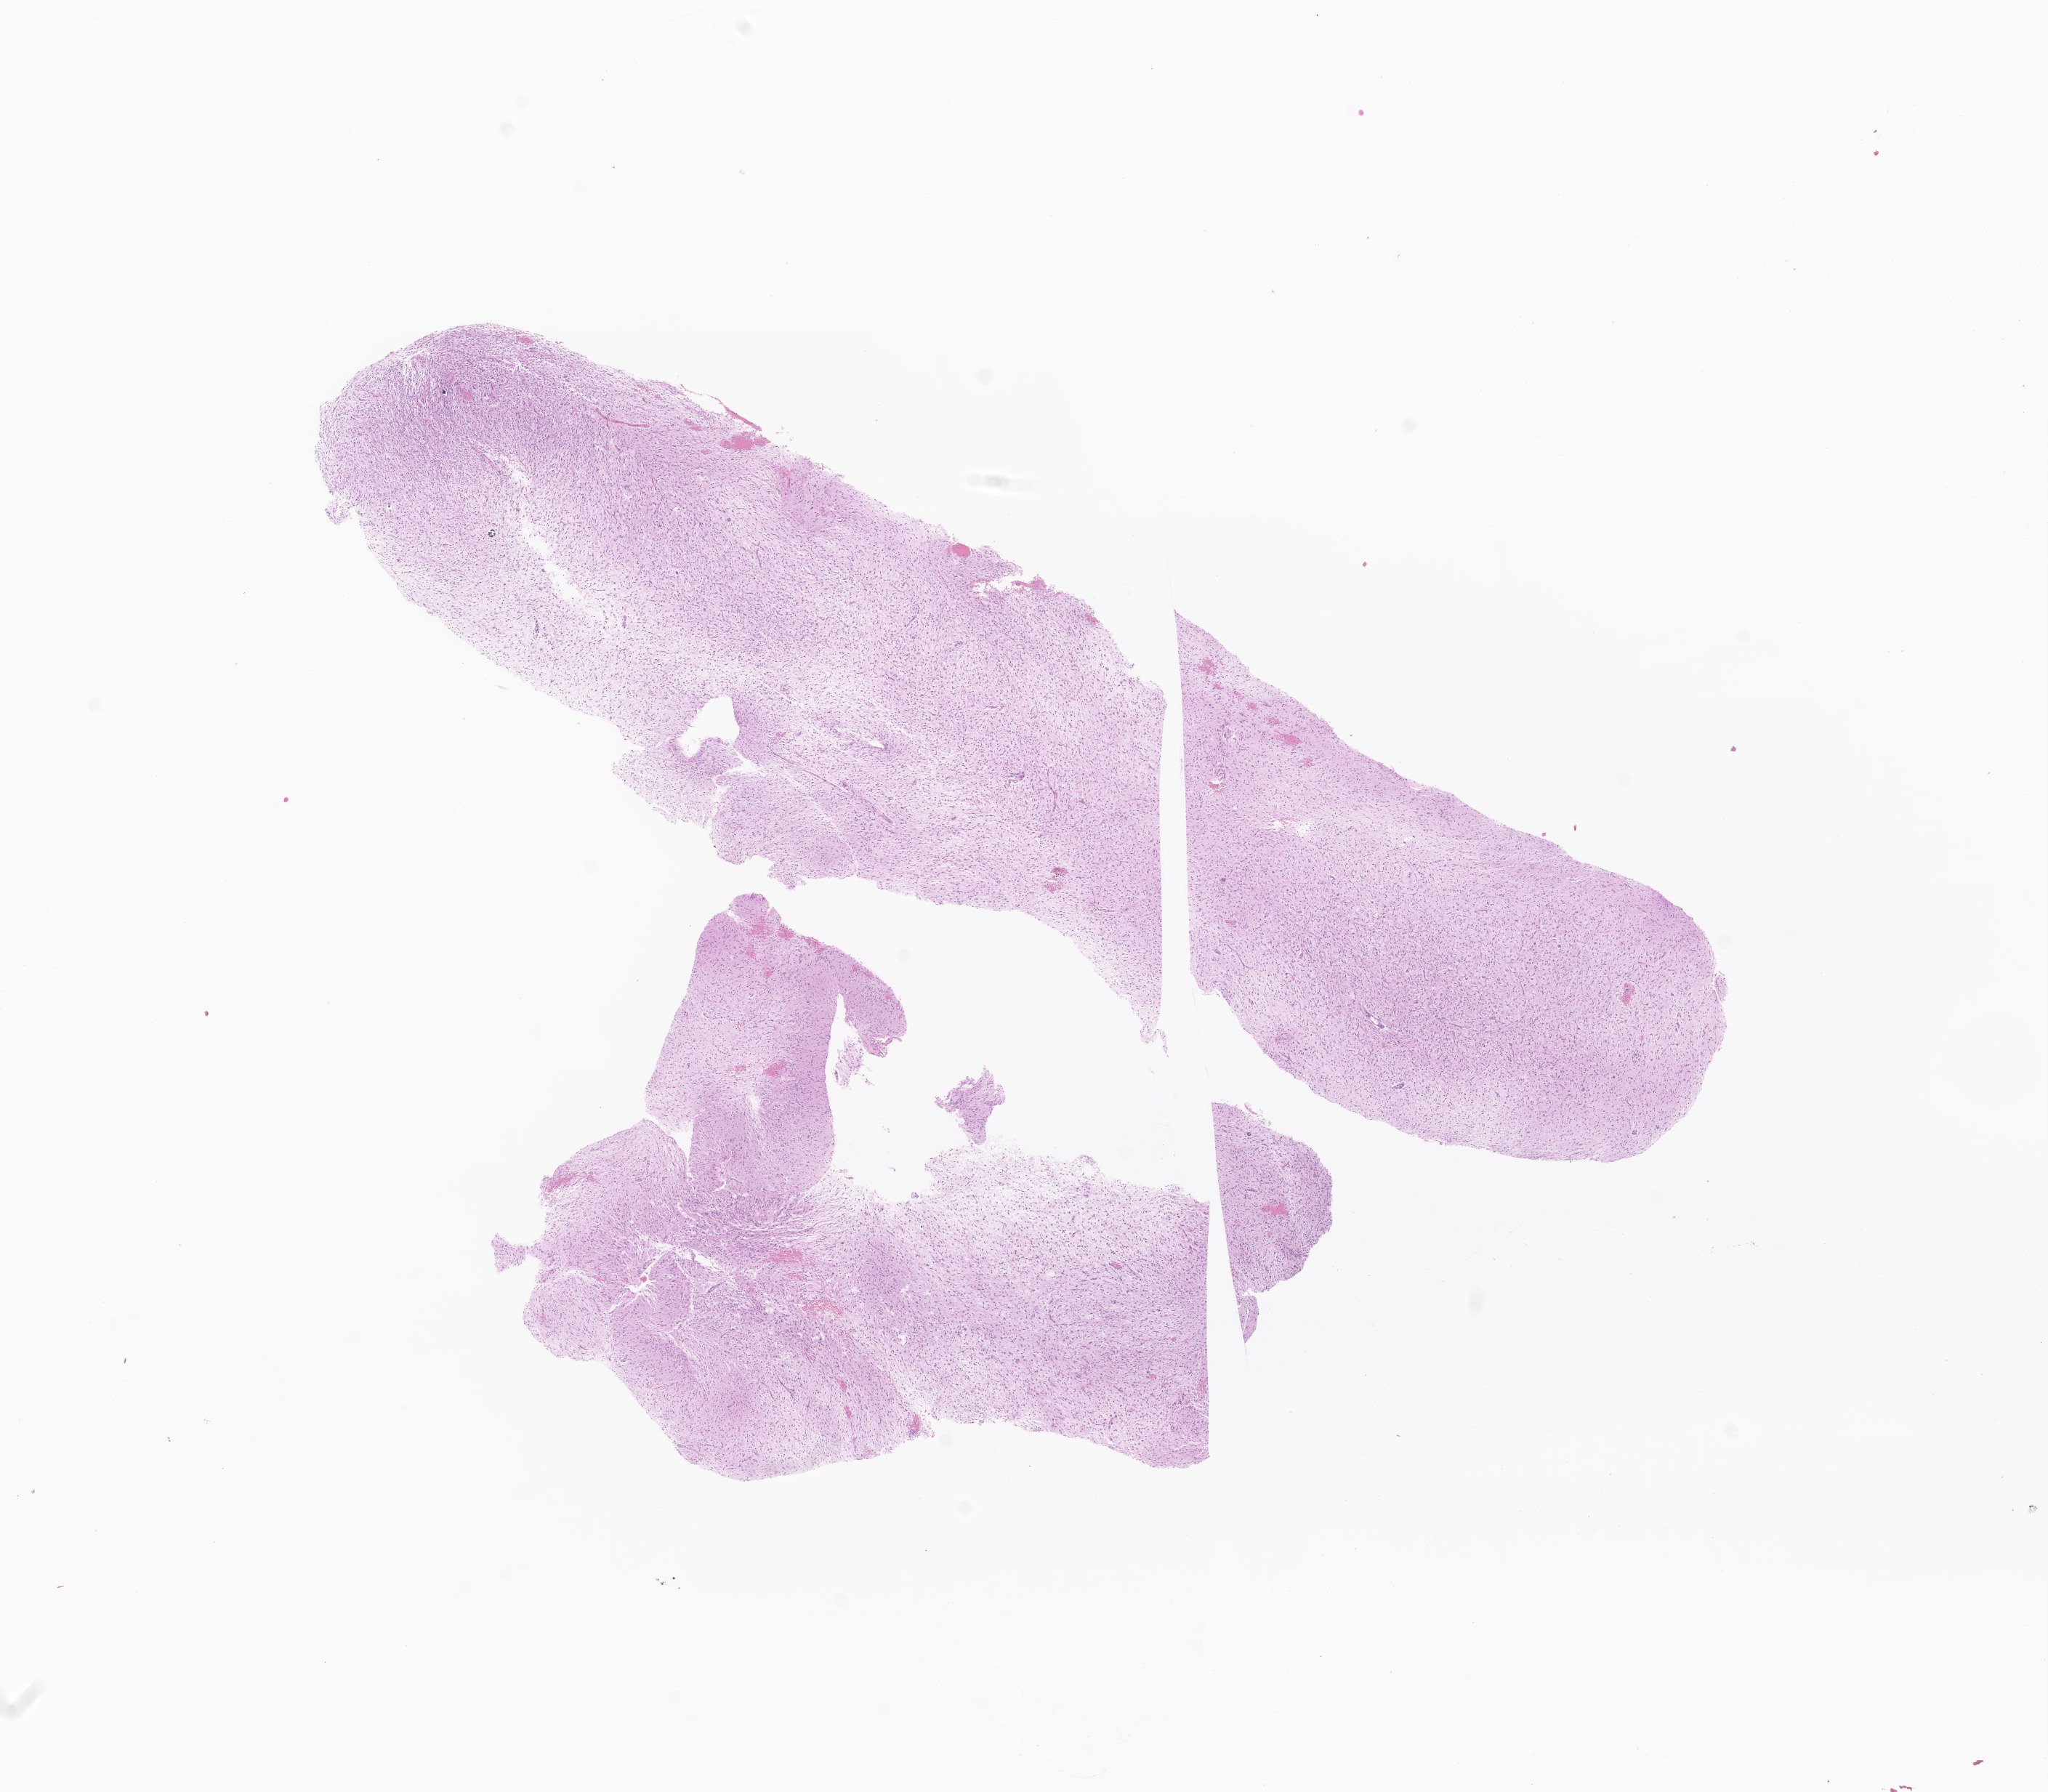
Whole-slide image, hematoxylin and eosin (H&E) stain of tumor tissue from the brain — a low-resolution overview of the entire scanned area, about 11.9 x 10.4 mm, formalin-fixed paraffin-embedded section. Patient: male, age 72 months (6 years).
• recorded diagnosis: Glioma, malignant